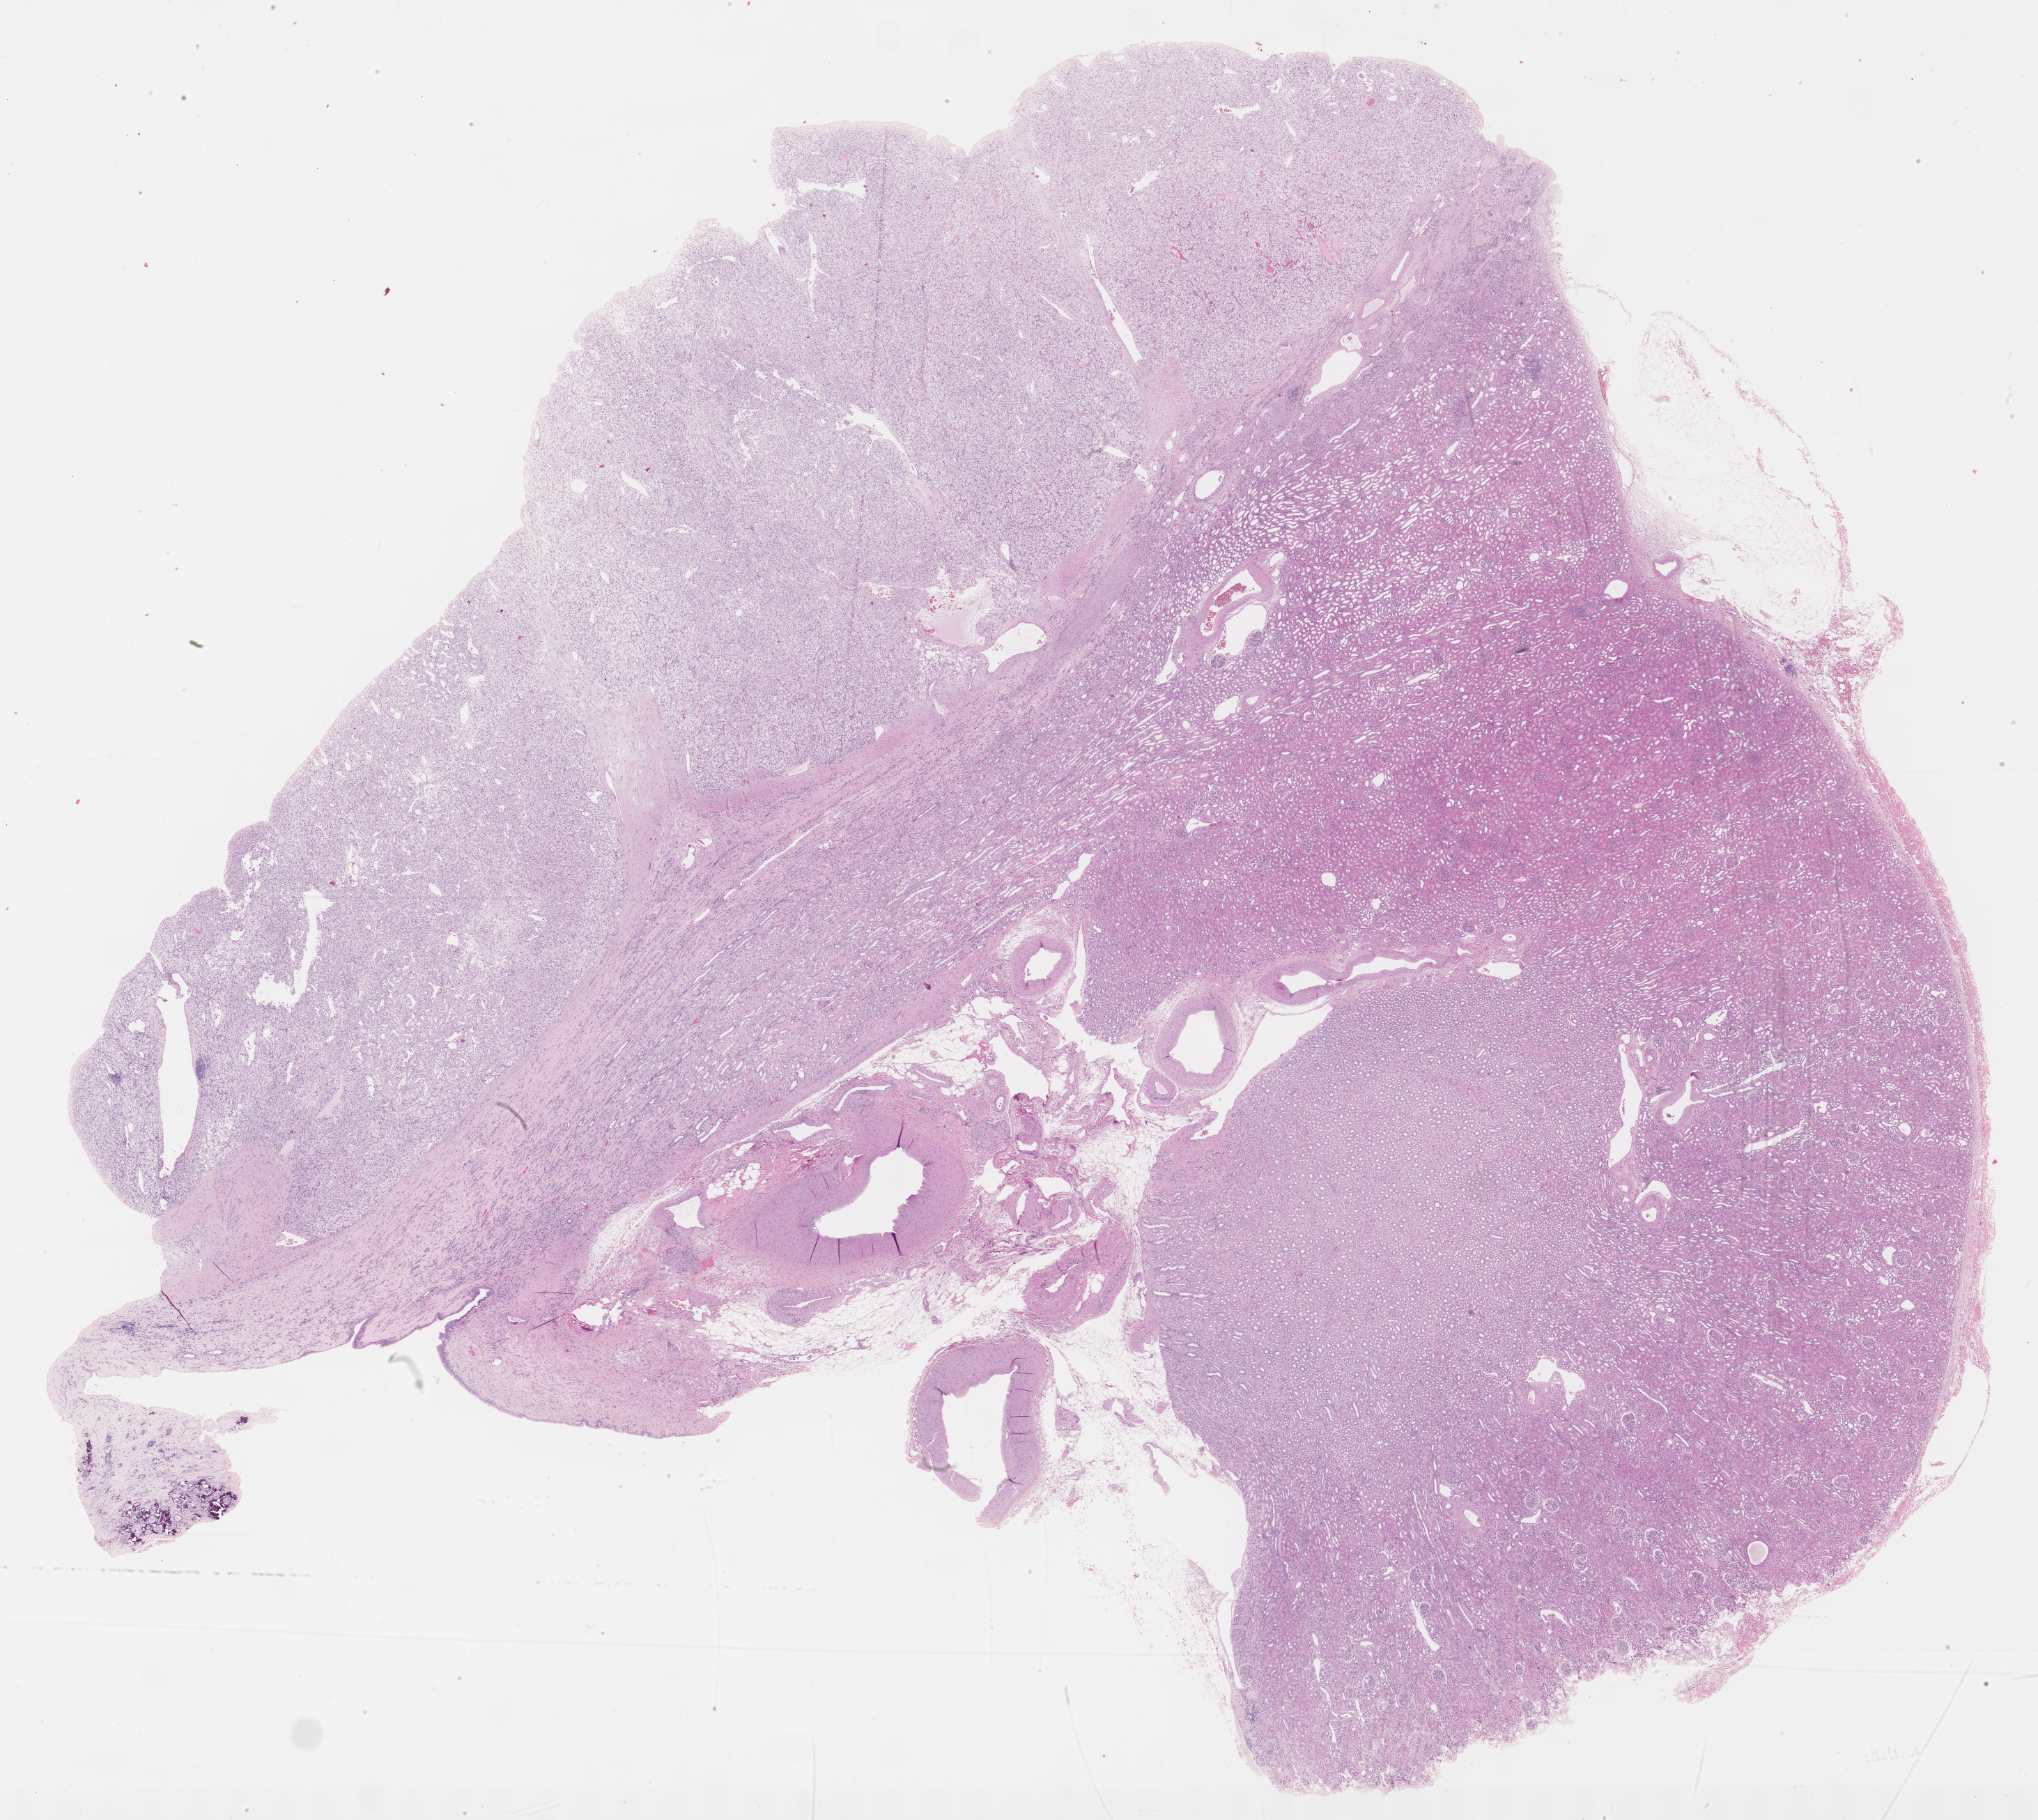
Whole-slide histology image, H&E-stained — low-resolution overview of the scanned area, about 23.6 x 21.1 mm (from a 40x scan); formalin-fixed paraffin-embedded (FFPE) diagnostic section; kidney, primary tumour sample. Female patient; age at initial diagnosis 63 years.
Histologic diagnosis: Clear cell adenocarcinoma, NOS.